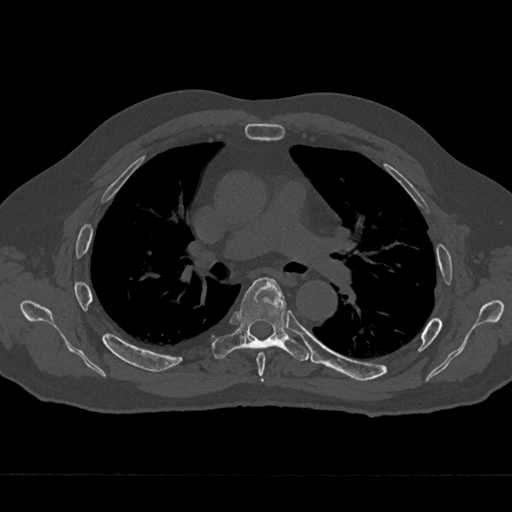
CT including the spine, one axial slice. Slice 439 of 797 in the series (ordered by position). Reconstruction kernel Br40s/3. Bone window (W 1800 / L 400 HU). 512 × 512 image matrix. Male patient, age 75 years. From the clinical record (not read from this slice): primary cancer: renal.
Structures marked on this image (semi-automatic segmentation, software-assisted and operator-edited):
- T5 vertebra: box from (x=256, y=352) to (x=266, y=382) px
- T6 vertebra: (x=213, y=277)–(x=309, y=361)